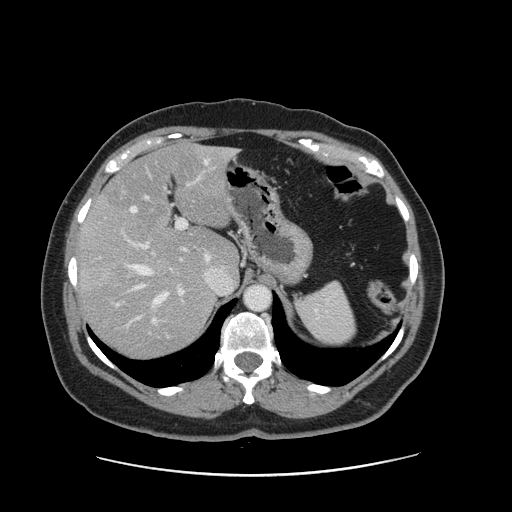
Contrast-enhanced abdominal CT, one axial slice; position 106 of 161 along the scan axis; 120 kVp; intravenous contrast given; soft-tissue window (W 400 / L 40 HU); 2.5 mm slice thickness; 512 × 512 image matrix, field of view 398 × 398 mm. Female patient, age 62 years. Case-level facts recorded for this patient, not image findings: diagnosis: colorectal cancer liver metastases, imaged before liver resection; multiple liver metastases: no; largest metastasis: 2.5 cm; disease in both lobes: no.
Outlined on this slice (outlined manually by an expert reader):
- hepatic veins: box from (x=129, y=150) to (x=235, y=322) px
- liver: (x=80, y=145)–(x=238, y=357)
- planned liver remnant (the part of the liver to remain after resection): (x=101, y=146)–(x=238, y=276)
- portal vein (with intrahepatic branches): (x=113, y=170)–(x=203, y=308)
- liver metastasis: (x=108, y=265)–(x=131, y=289)